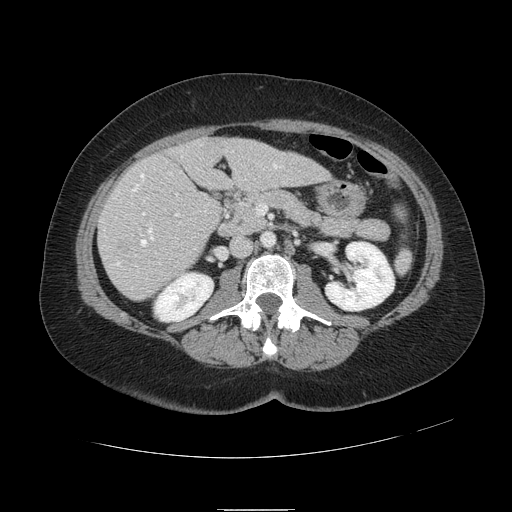
Contrast-enhanced abdominal CT, one axial slice. Position 39 of 121 along the scan axis. Intravenous contrast given. Soft-tissue window (W 400 / L 40 HU). 2.5 mm slice thickness. 512 × 512 image matrix, field of view 400 × 400 mm. Female patient, age 52 years. Case-level facts recorded for this patient, not image findings: diagnosis: colorectal cancer liver metastases, imaged before liver resection; multiple liver metastases: yes; largest metastasis: 6.3 cm.
Outlined on this slice (expert manual segmentation):
- hepatic veins: box from (x=117, y=165) to (x=278, y=265) px
- liver: (x=100, y=137)–(x=329, y=300)
- planned liver remnant (the part of the liver to remain after resection): (x=178, y=137)–(x=329, y=191)
- portal vein (with intrahepatic branches): (x=143, y=194)–(x=179, y=216)